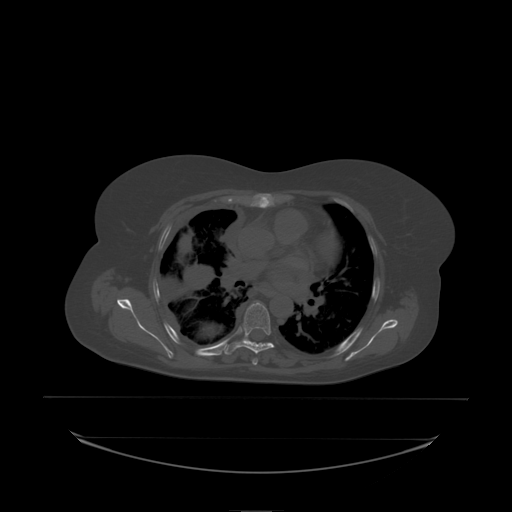
CT including the spine, one axial slice. Position 151 of 242 along the scan axis. Bone window (W 1800 / L 400 HU). 2.5 mm slice thickness. 512 × 512 image matrix, field of view 500 × 500 mm. Female patient, age 53 years. Case-level facts recorded for this patient, not image findings: primary cancer: lung.
Annotated regions visible in this slice (semi-automatically segmented with operator editing):
- T6 vertebra: bounding box (x1, y1, x2, y2) in pixels: (244, 303, 271, 337)